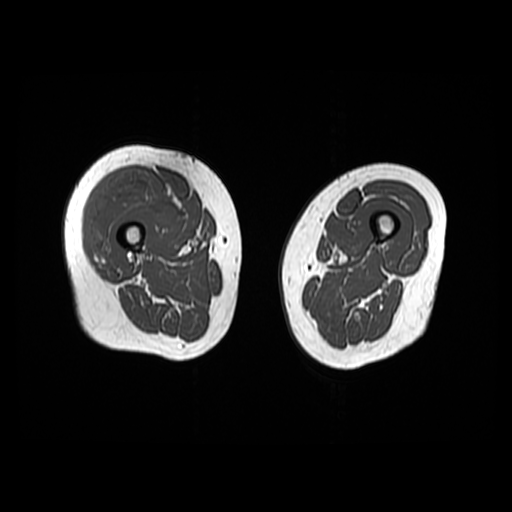
MRI of an extremity soft-tissue mass, one axial slice; 6 mm slice thickness; 512 × 512 image matrix, field of view 440 × 440 mm. Female patient. From the clinical record (not read from this slice): histological type: pleiomorphic undifferentiated sarcoma; grade: high; site of the primary tumour: right quadricep.
Structures marked on this image (manually delineated by an expert):
- gross tumour volume including surrounding oedema: box from (x=86, y=174) to (x=181, y=264) px
- gross tumour volume (mass): (x=86, y=174)–(x=181, y=264)